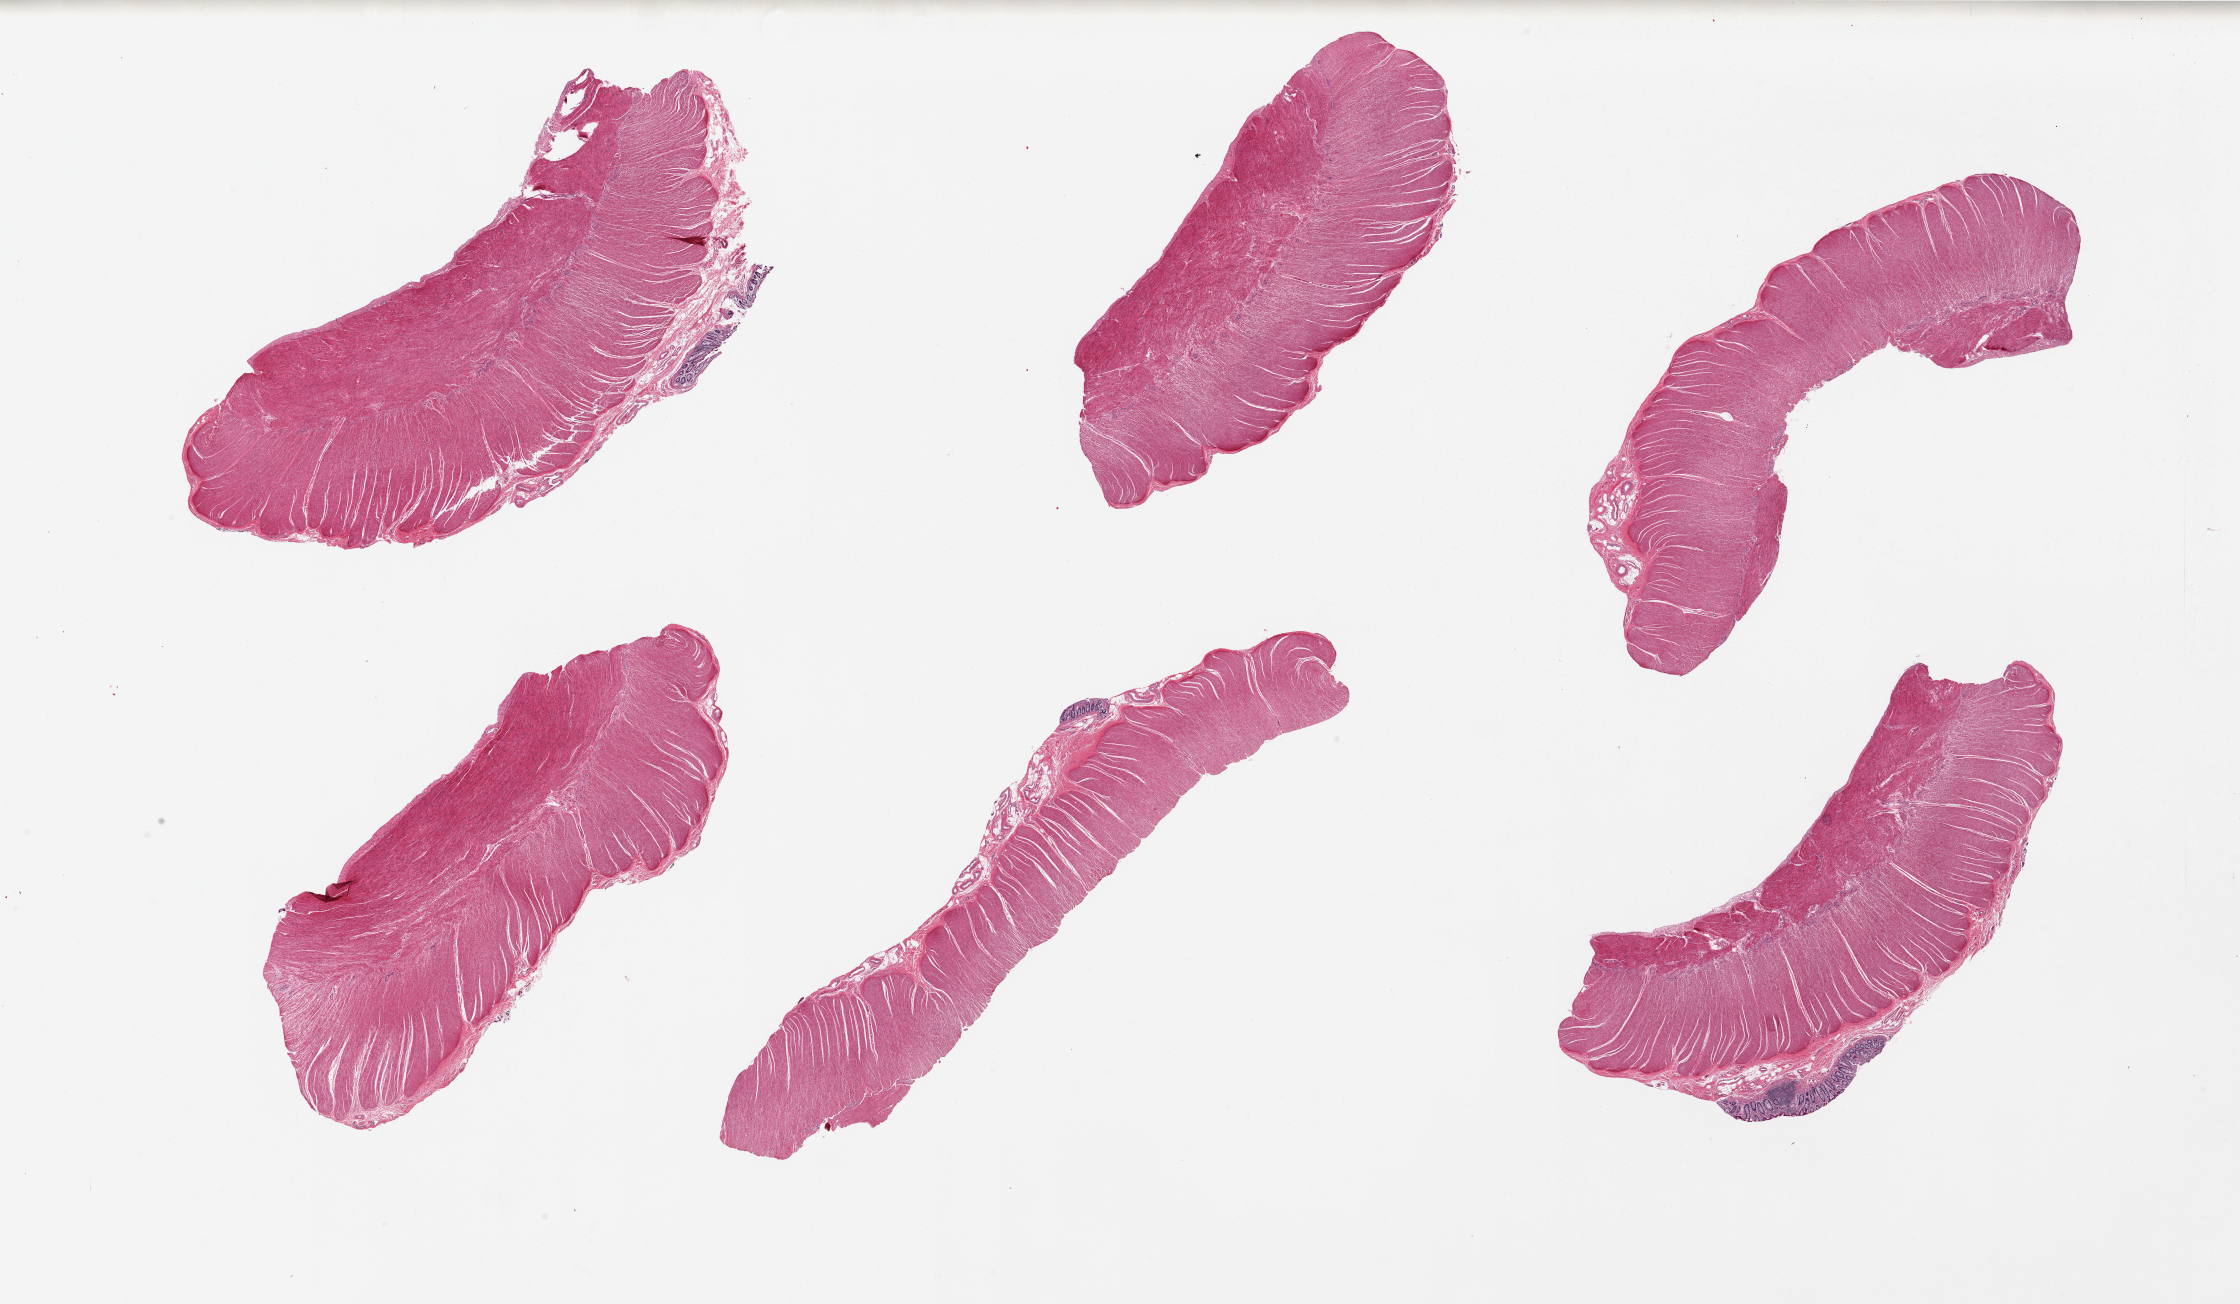
Digitized H&E-stained section, whole scanned area (about 35.4 x 20.6 mm, slide scanned at 20x) shown as a low-resolution overview. PAXgene-fixed paraffin-embedded (PFPE) section. Sampled site (target tissue): sigmoid colon. Tissue donor sample. Donor: male.
* review note (as recorded): 6 pieces; 3 with small regions of residual mucosa (not fully trimmed)